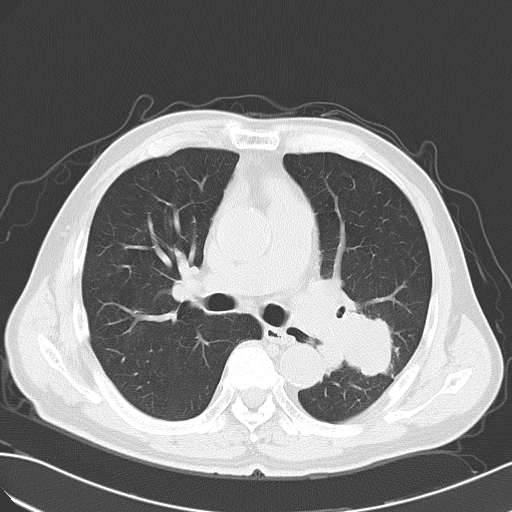
Chest CT, one axial slice; position 33 of 55 along the scan axis; lung window (W 1500 / L -600 HU); 512 × 512 image matrix. Patient: male, 63 years. From the clinical record (not read from this slice): clinical TNM (as recorded): T3 N3 M1a.
Outlined on this slice (bounding box drawn by a radiologist):
- lung tumour (recorded histology: large cell carcinoma): bounding box <302,291,401,385> (left, top, right, bottom; pixels)